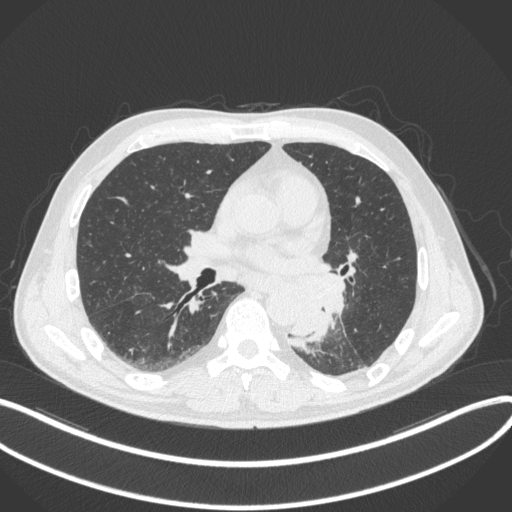
Chest CT, one axial slice; position 168 of 328 along the scan axis; lung window (W 1500 / L -600 HU); 512 × 512 image matrix. Male patient, age 59 years. Case-level facts recorded for this patient, not image findings: clinical TNM (as recorded): T2a N2 M0.
Outlined on this slice (bounding box drawn by a radiologist):
- lung tumour (recorded histology: squamous cell carcinoma): box from (x=288, y=275) to (x=348, y=344) px